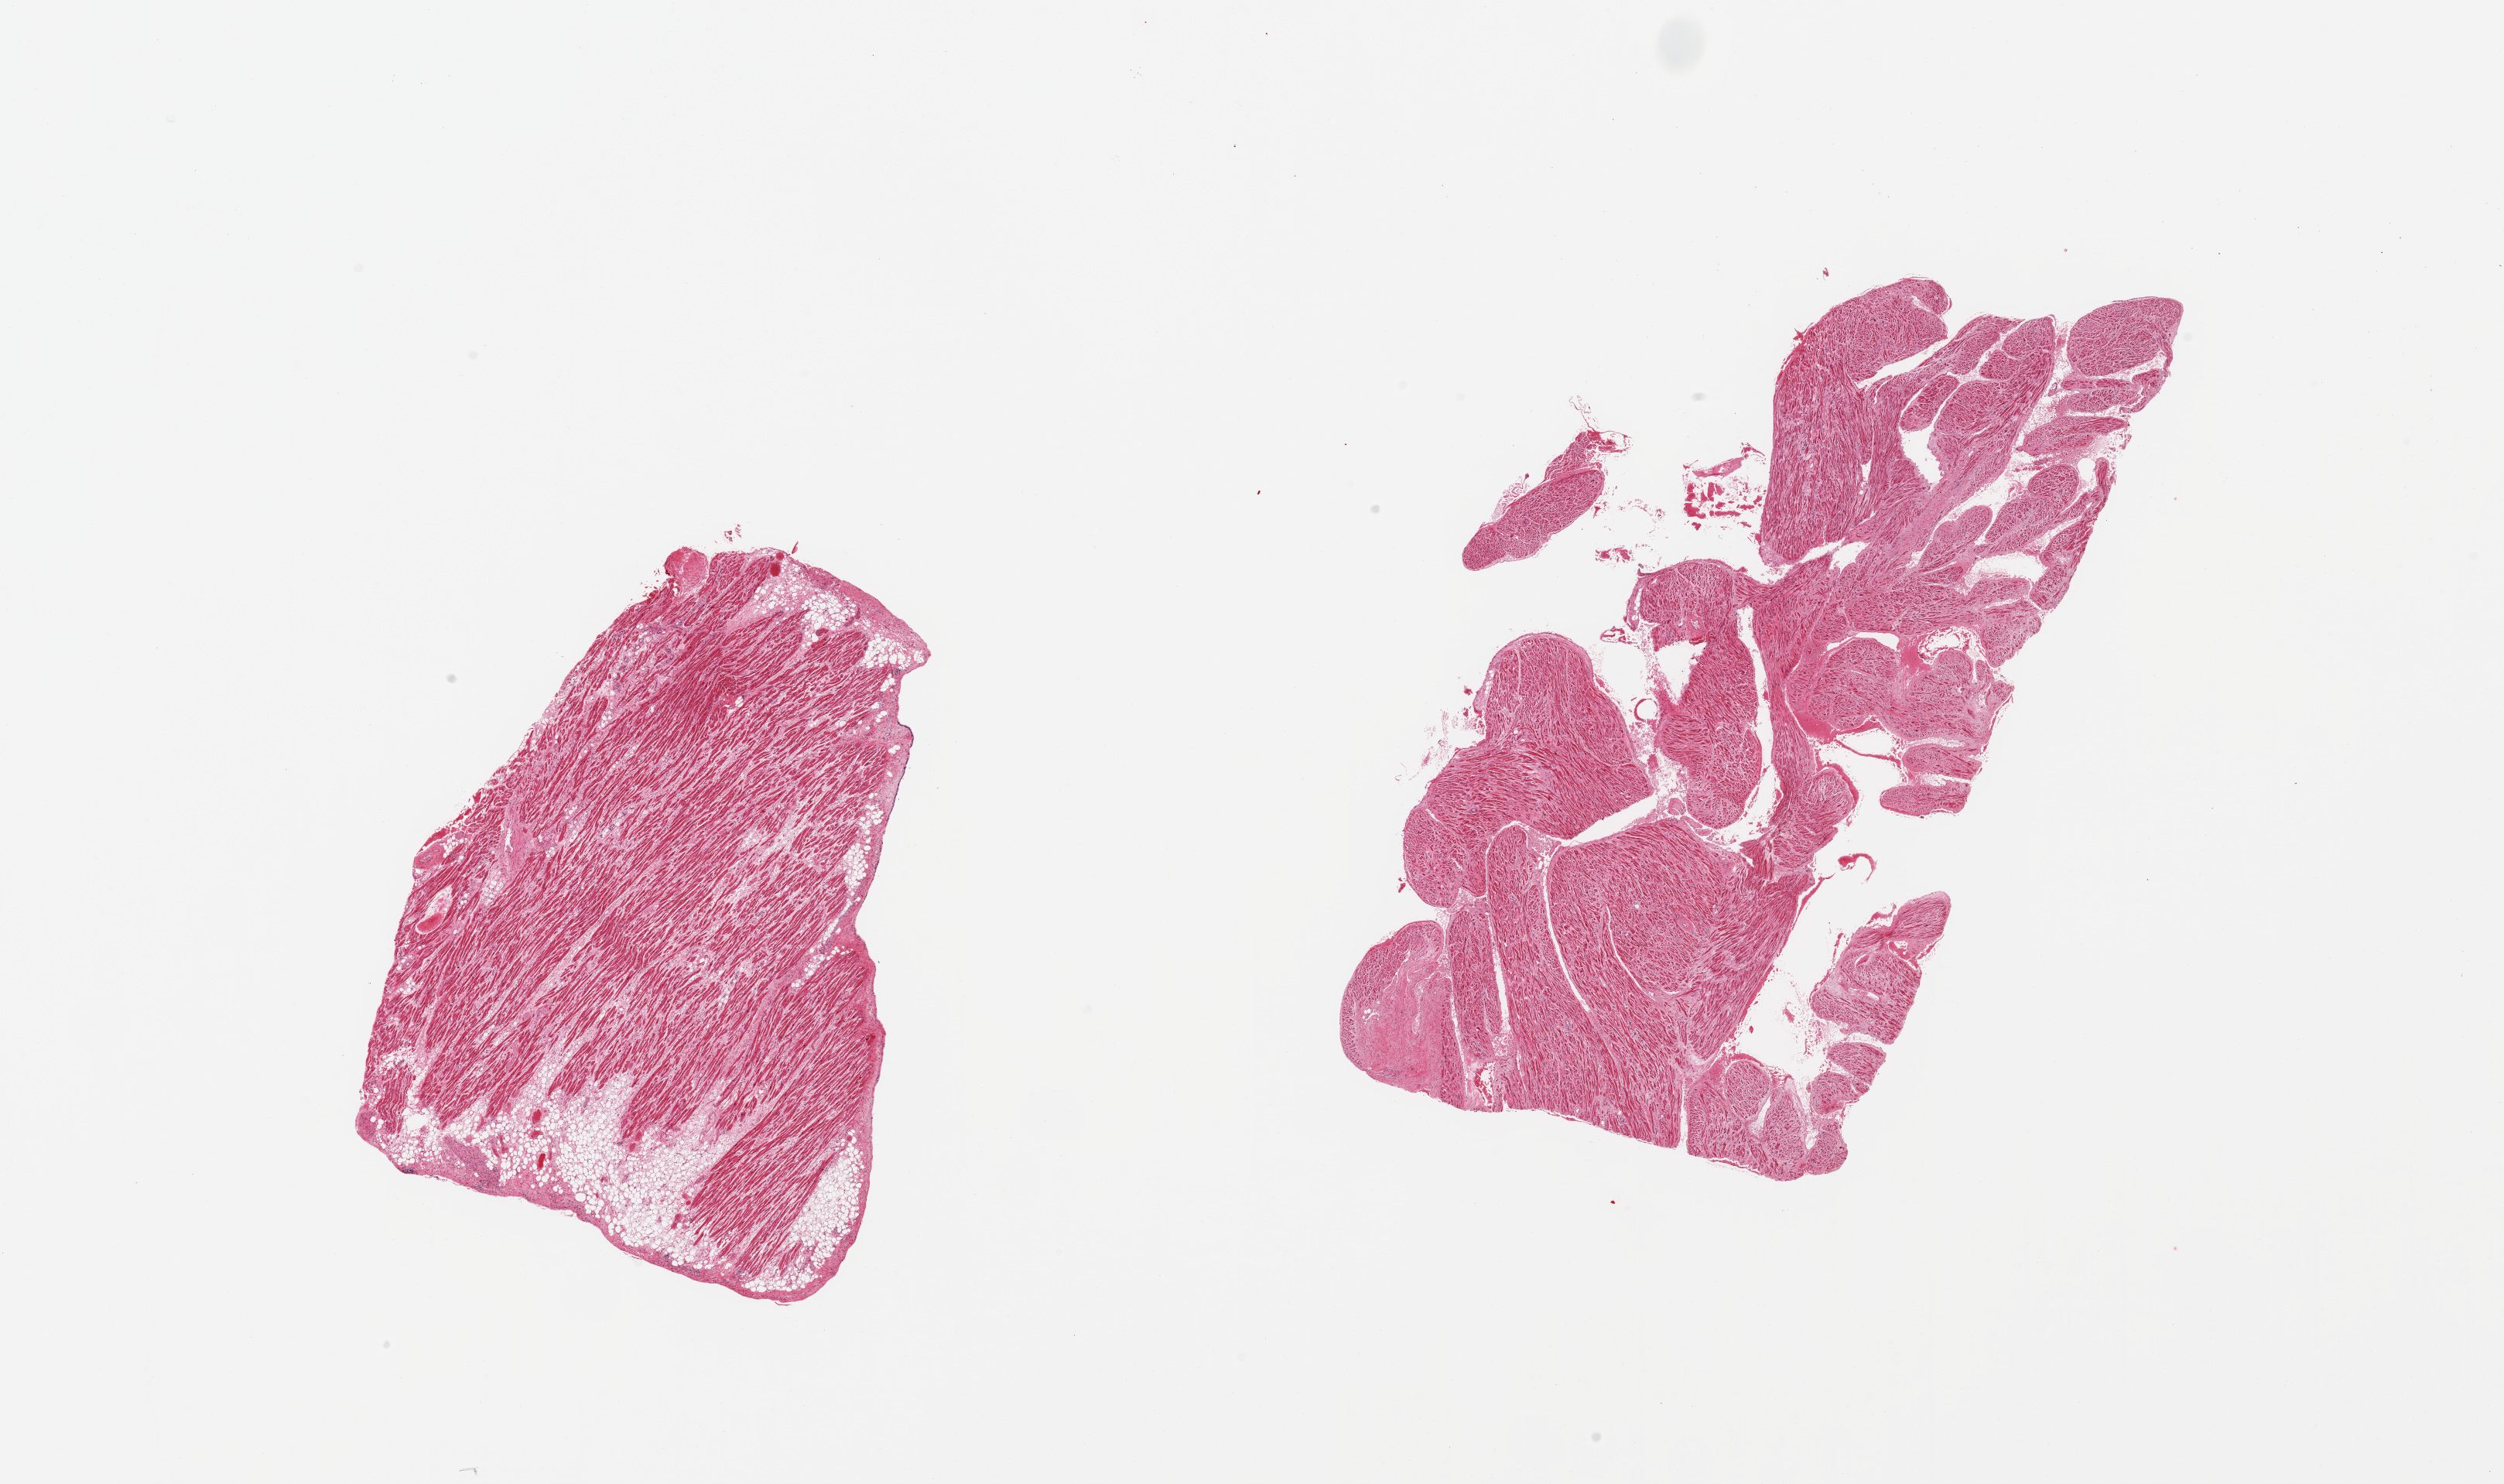
Digitized hematoxylin and eosin (H&E)-stained section, shown as a low-resolution overview of the whole scanned area (about 25.6 x 15.2 mm); PAXgene-fixed, paraffin-embedded tissue; target tissue: auricular appendage; donor tissue sample. Donor: female.
* pathologist's review note for this sample: 2 pieces, no abnormalities